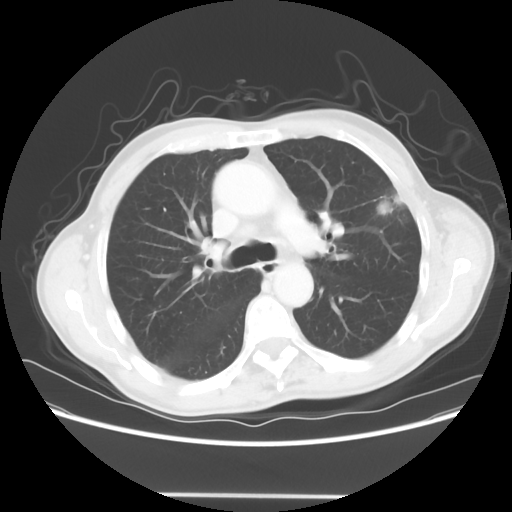
Chest CT, one axial slice; slice 41 of 64 in the series (ordered by position); reconstruction kernel STANDARD; 120 kVp; lung window (W 1500 / L -600 HU); 5 mm slice thickness; 512 × 512 image matrix, field of view 392 × 392 mm. Male patient, age 71 years. From the clinical record (not read from this slice): clinical TNM (as recorded): T1c N0 M0; histopathological grade: G2-3.
Outlined on this slice (bounding box drawn by a radiologist):
- lung tumour (recorded histology: adenocarcinoma): bounding box [x1, y1, x2, y2] px = [373, 186, 407, 221]